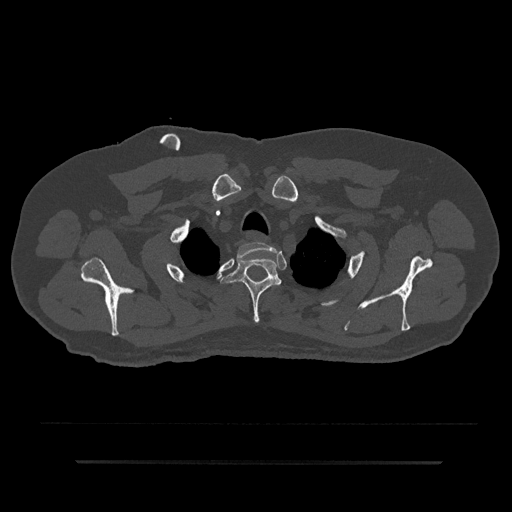
CT including the spine, one axial slice; reconstruction kernel Br40s/3; 120 kVp; bone window (W 1800 / L 400 HU); 0.5 mm slice thickness; 512 × 512 image matrix. Male patient, age 59 years. Case-level facts recorded for this patient, not image findings: primary cancer: bile ducts.
Structures marked on this image (semi-automatically segmented with operator editing):
- T1 vertebra: bounding box [x1, y1, x2, y2] px = [238, 242, 276, 259]
- T2 vertebra: [221, 255, 281, 324]